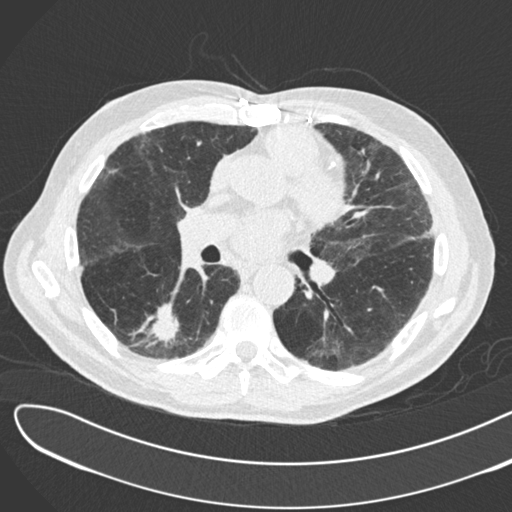
Axial slice from a low-dose chest CT screening exam. Second annual screen. Lung window (W 1500 / L -600 HU). 2 mm slice thickness. Standard (soft-tissue) reconstruction kernel (B30f). 512 × 512 image matrix, field of view 370 × 370 mm. Male, age 72 years at enrolment. Former smoker at enrolment.
• Expert reader's lesion annotation, bounding box (x1, y1, x2, y2) in pixels: (133, 291, 194, 349).
• The screening reader recorded 2 non-calcified nodules or masses ≥4 mm on this exam; which of them this box marks is not recorded.
• Official screen result: positive, change unspecified: nodule(s) >= 4 mm or enlarging nodule(s), mass(es), or other non-specific abnormalities suspicious for lung cancer.
• Participant outcome: lung cancer diagnosed 46 days after this screen — squamous cell carcinoma, NOS, right lower lobe, poorly differentiated (G3), stage IB (AJCC 6th edition), 42 mm at pathology.